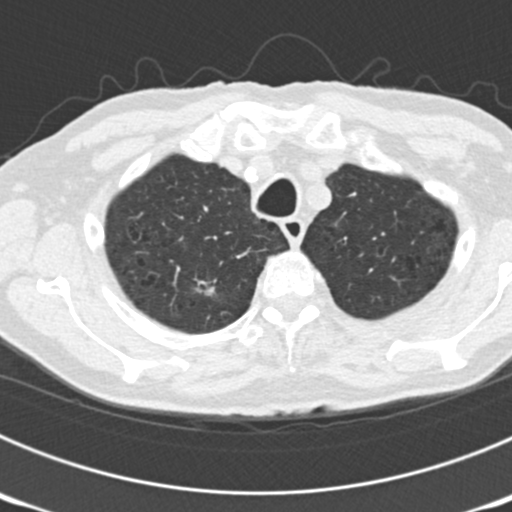
Low-dose screening chest CT, one axial slice. Position 153 of 177 along the scan axis. Reconstruction kernel B30f. Lung window (W 1500 / L -600 HU). 2 mm slice thickness. 512 × 512 image matrix.
Outlined on this slice (expert manual segmentation):
- lesion 3 (nodule, upper lobe of right lung): bounding box <196,279,217,295> (left, top, right, bottom; pixels)